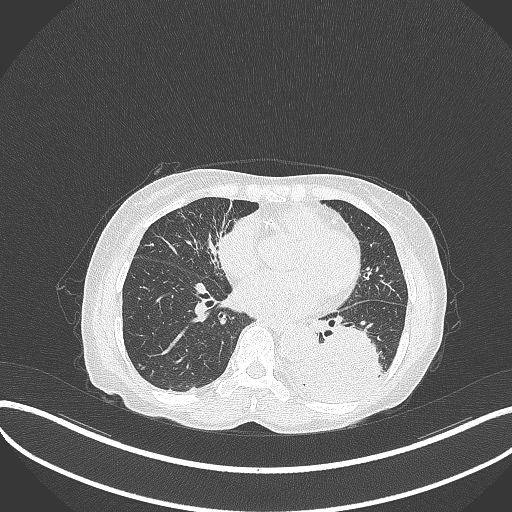
Chest CT, one axial slice. Slice 128 of 370 in the series (ordered by position). Reconstruction kernel B70f. 120 kVp. Lung window (W 1500 / L -600 HU). 512 × 512 image matrix, field of view 400 × 400 mm. Female patient, age 78 years. From the clinical record (not read from this slice): clinical TNM (as recorded): T3 N0 M1.
Annotated regions visible in this slice (rectangle marked by the reading radiologist):
- lung tumour (recorded histology: squamous cell carcinoma): bounding box (x1, y1, x2, y2) in pixels: (289, 325, 385, 404)